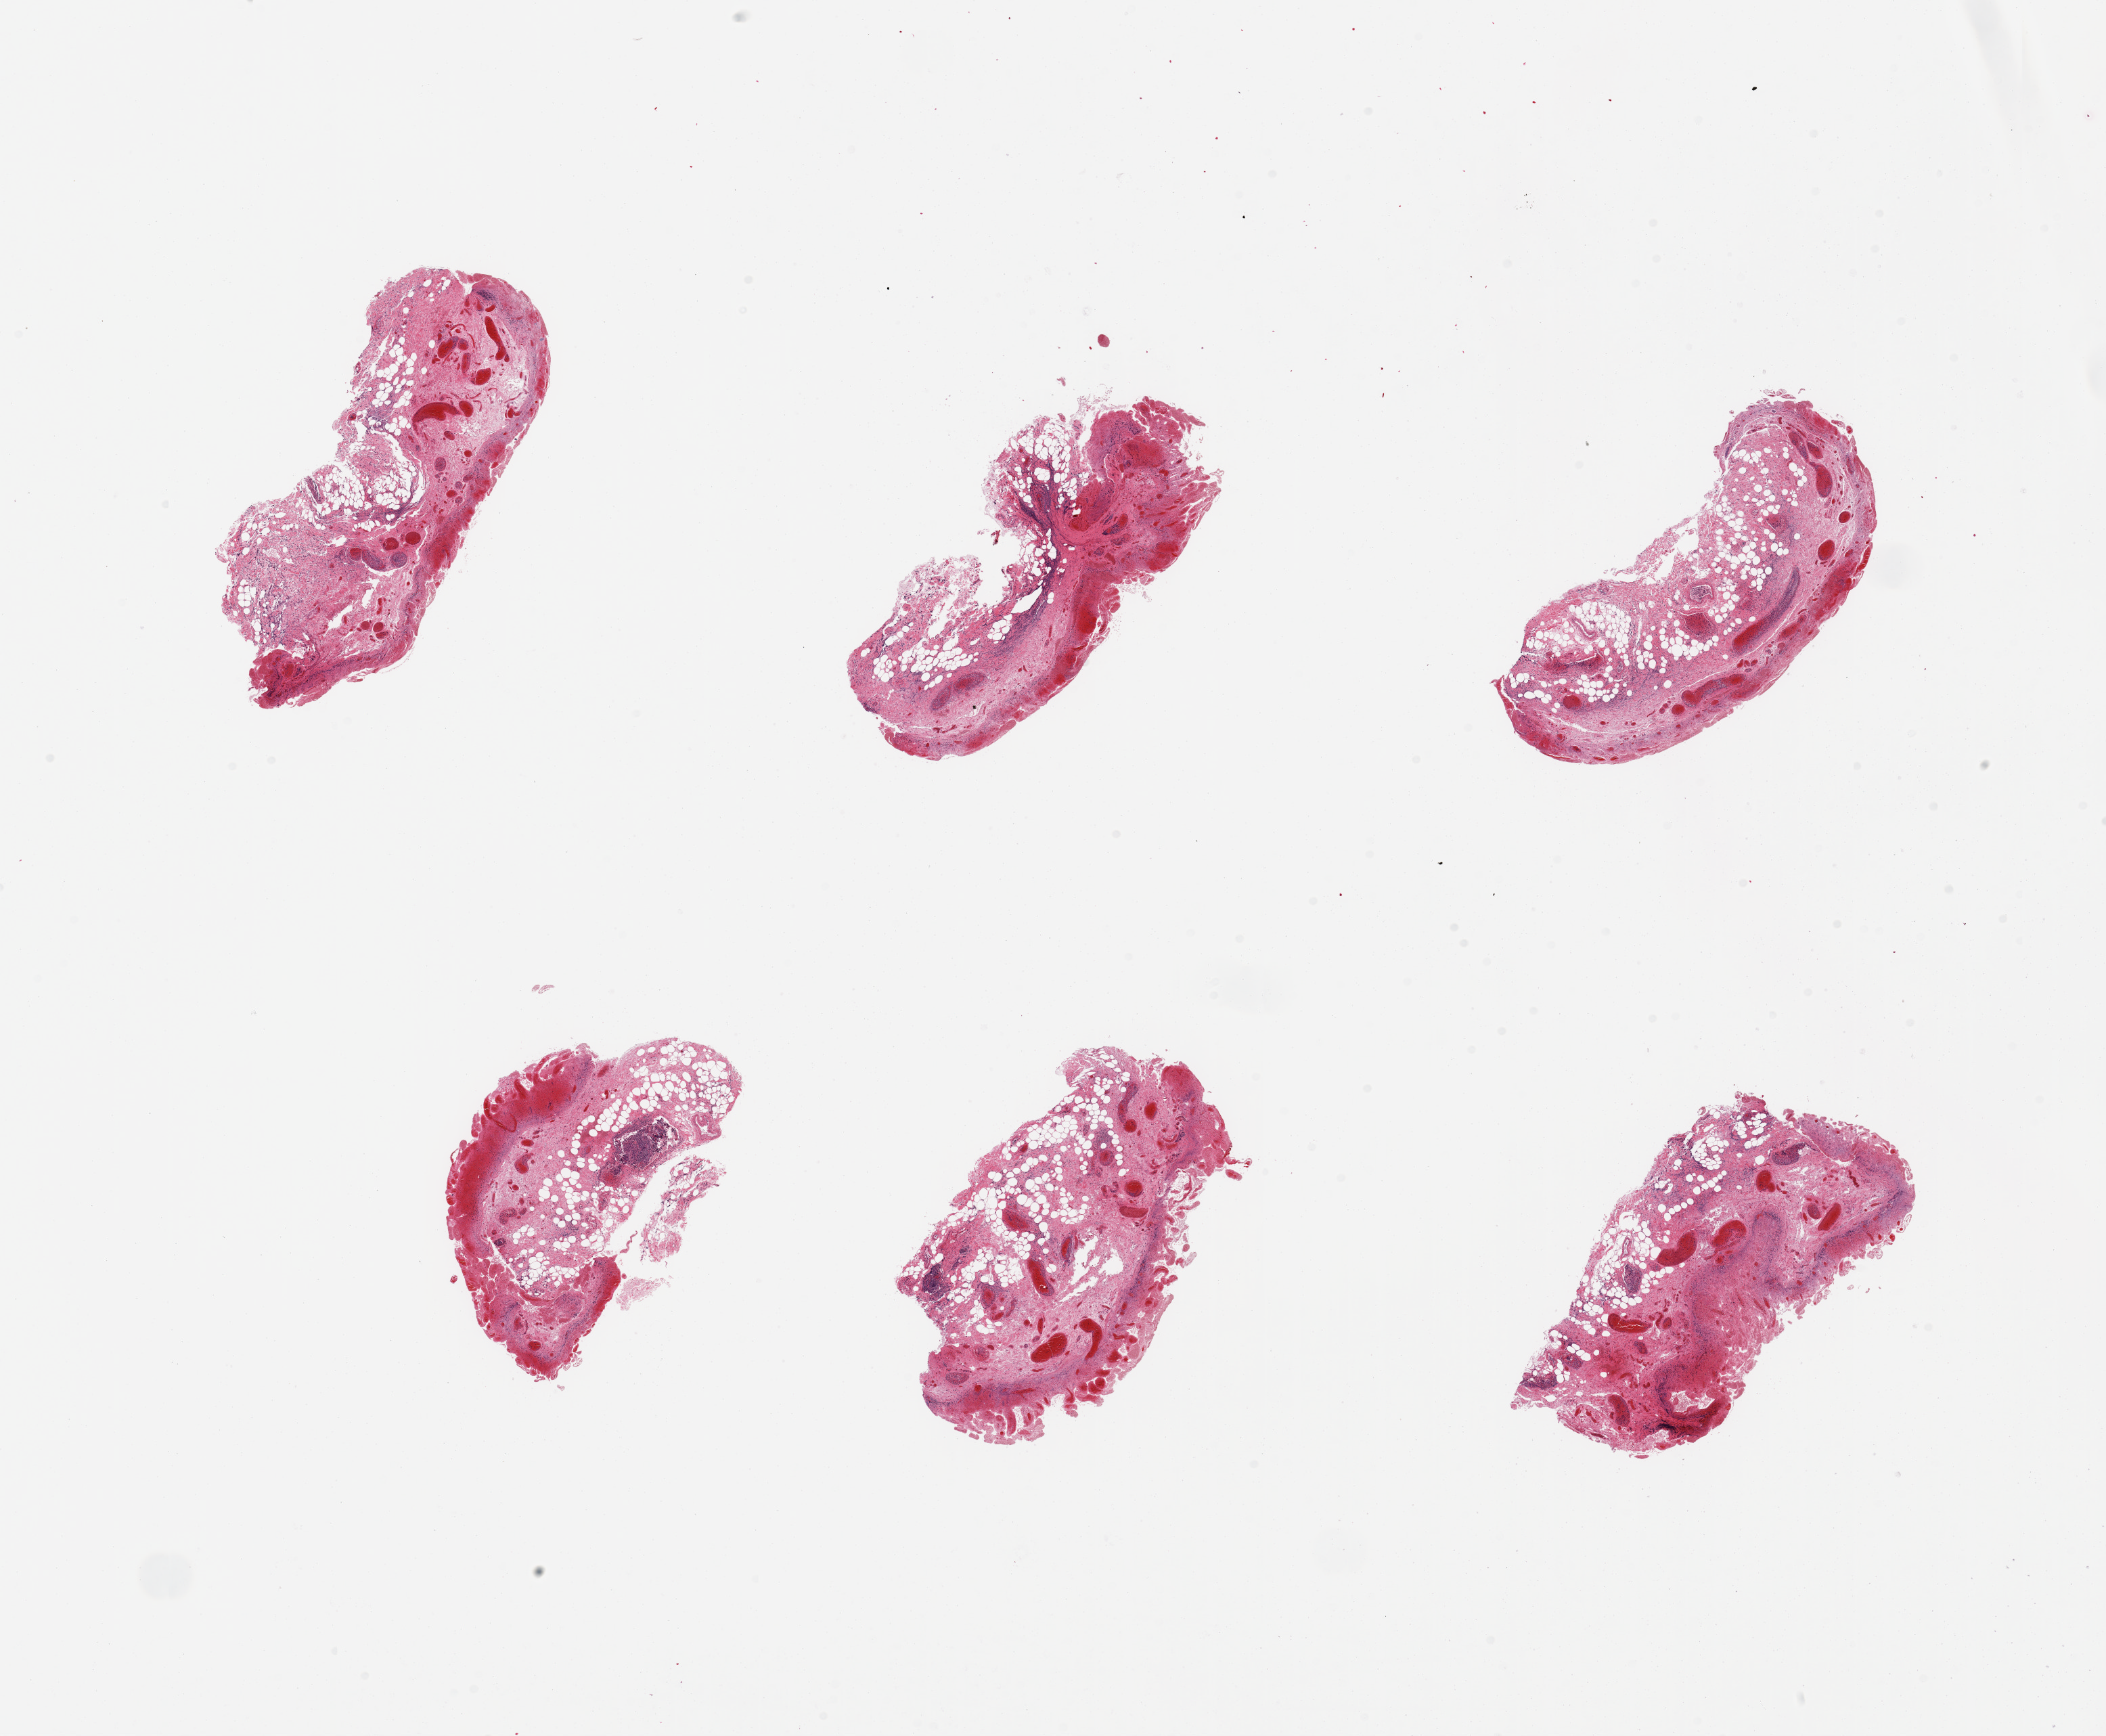
Digitized H&E-stained section, a low-resolution overview of the entire scanned area, about 24.6 x 20.3 mm; PAXgene-fixed, paraffin-embedded tissue; target tissue: ileum; donor tissue sample. Male donor.
Reviewer comment on this tissue sample: 4 pieces, mucosa autolyzed, correct target but too little lymphoid tissue for analysis.